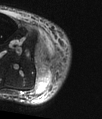
MRI of an extremity soft-tissue mass, one axial slice. T2-weighted fat-saturated. MR volume resampled by the dataset authors to the PET/CT grid (not the native acquisition matrix). 102 × 119 image matrix, field of view 100 × 116 mm. Male patient. From the clinical record (not read from this slice): histological type: pleiomorphic liposarcoma; grade: high; site of the primary tumour: right calf.
Annotated regions visible in this slice (expert contour drawn on MRI and transferred to this co-registered scan by the dataset authors):
- gross tumour volume including surrounding oedema: box from (x=35, y=40) to (x=59, y=79) px